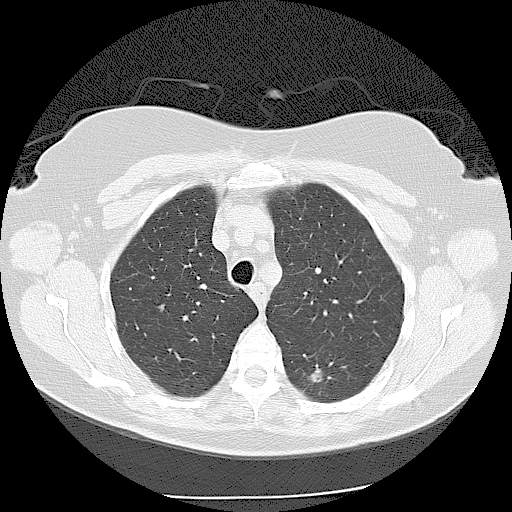
Chest CT (low-dose screening protocol), one axial image, second screening round (one year after baseline), lung window (W 1500 / L -600 HU), 2.5 mm slice thickness, slice 30 of 116 in the series. Female, age 56 years at enrolment.
Expert reader's lesion annotation, bounding box <290,347,352,408> (left, top, right, bottom; pixels). The exam's reader record, not a measurement of the box and not confirmed to be the same lesion: non-calcified nodule or mass ≥4 mm, left lower lobe, 9 × 9 mm, spiculated (stellate) margins, soft tissue attenuation, pre-existing on the prior screen: yes; interval growth: yes. Later outcome: lung cancer diagnosed 173 days after this screen — adenocarcinoma, NOS, left lower lobe, moderately differentiated (G2), stage IIA (AJCC 6th edition), 15 mm at pathology.